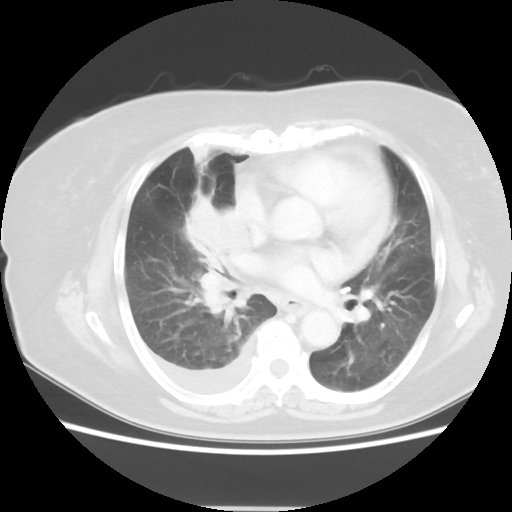
Chest CT, one axial slice; position 25 of 48 along the scan axis; reconstruction kernel STANDARD; 120 kVp; lung window (W 1500 / L -600 HU); 512 × 512 image matrix, field of view 360 × 360 mm. Patient: female, 73 years. From the clinical record (not read from this slice): clinical TNM (as recorded): T3 N3 M1b.
Outlined on this slice (bounding box drawn by a radiologist):
- lung tumour (recorded histology: small cell carcinoma): bounding box <184,197,252,310> (left, top, right, bottom; pixels)